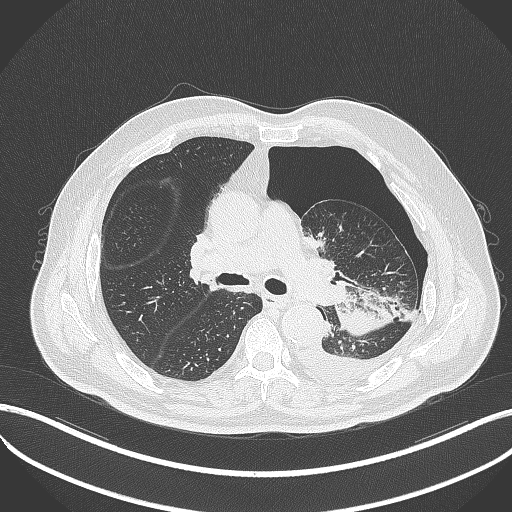
Chest CT, one axial slice. Reconstruction kernel B70f. 120 kVp. Lung window (W 1500 / L -600 HU). 1 mm slice thickness. 512 × 512 image matrix, field of view 400 × 400 mm. Male patient, age 76 years. Case-level facts recorded for this patient, not image findings: clinical TNM (as recorded): T3 N0 M1b.
Annotated regions visible in this slice (rectangle marked by the reading radiologist):
- lung tumour (recorded histology: adenocarcinoma): box from (x=326, y=293) to (x=397, y=336) px